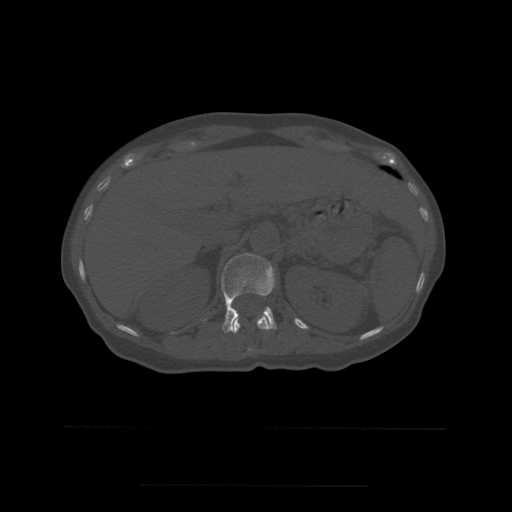
CT including the spine, one axial slice. Position 245 of 544 along the scan axis. Bone window (W 1800 / L 400 HU). 1.25 mm slice thickness. 512 × 512 image matrix, field of view 350 × 350 mm. Patient age 58 years. Case-level facts recorded for this patient, not image findings: primary cancer: lung.
Annotated regions visible in this slice (semi-automatic segmentation, software-assisted and operator-edited):
- L1 vertebra: bounding box (x1, y1, x2, y2) in pixels: (221, 254, 277, 333)
- T12 vertebra: (233, 316, 270, 351)